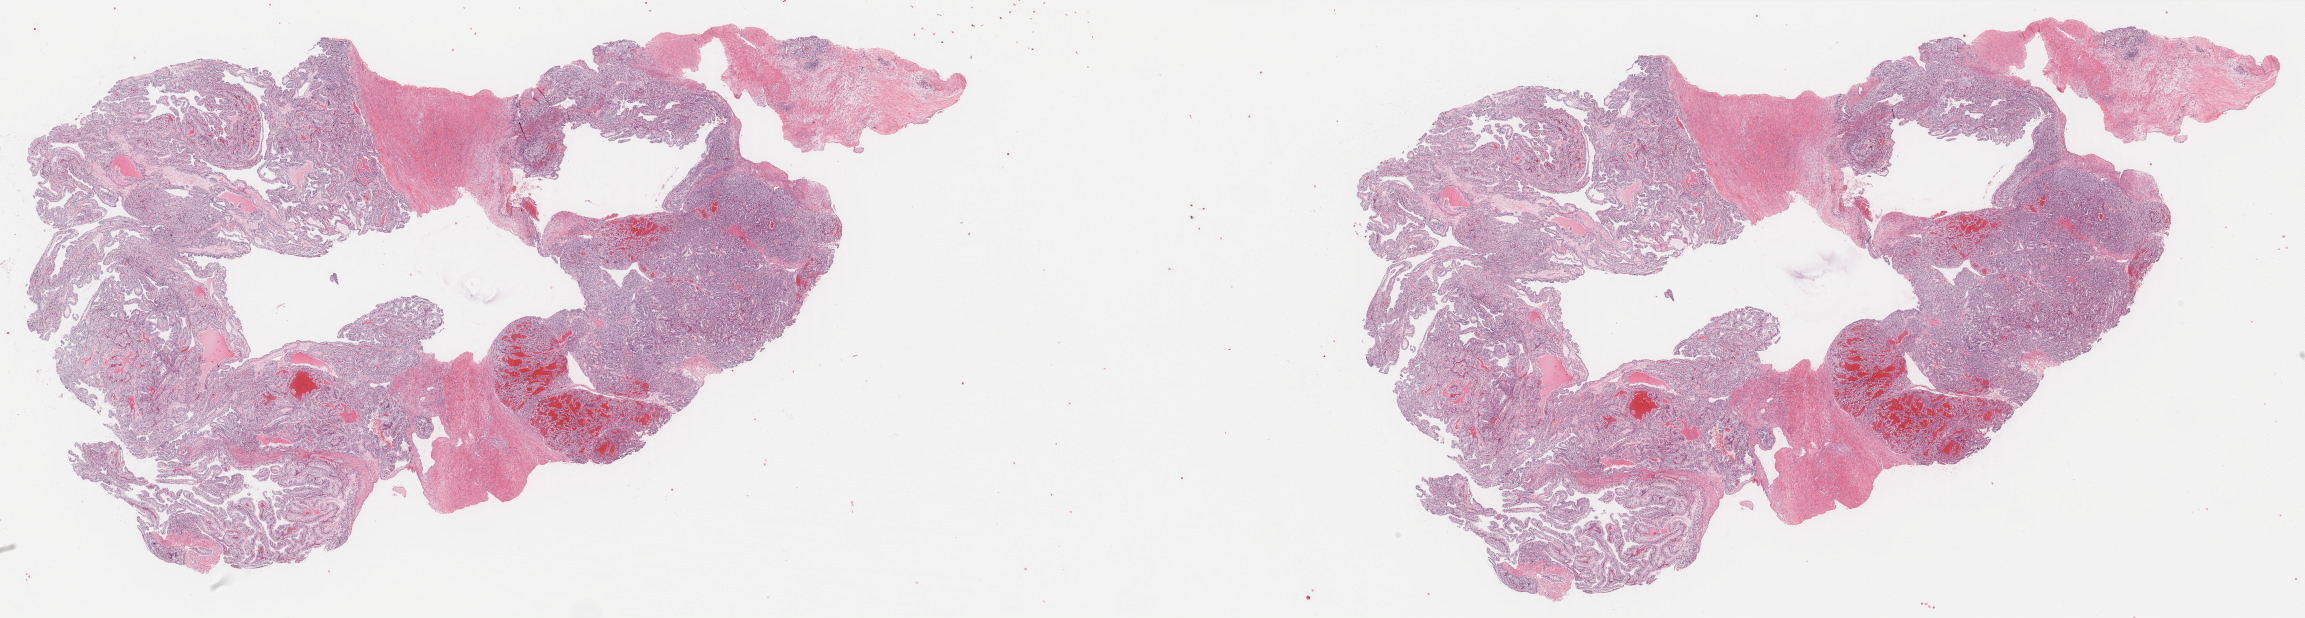
H&E whole-slide image, low-resolution overview of the scanned area, about 36.5 x 9.8 mm; FFPE section; sample: primary tumour, kidney. Male, age 69 years at initial diagnosis. Histologic grade: G2 (moderately differentiated).
* AJCC pathologic stage: III
* pathologic diagnosis: Renal cell carcinoma, NOS